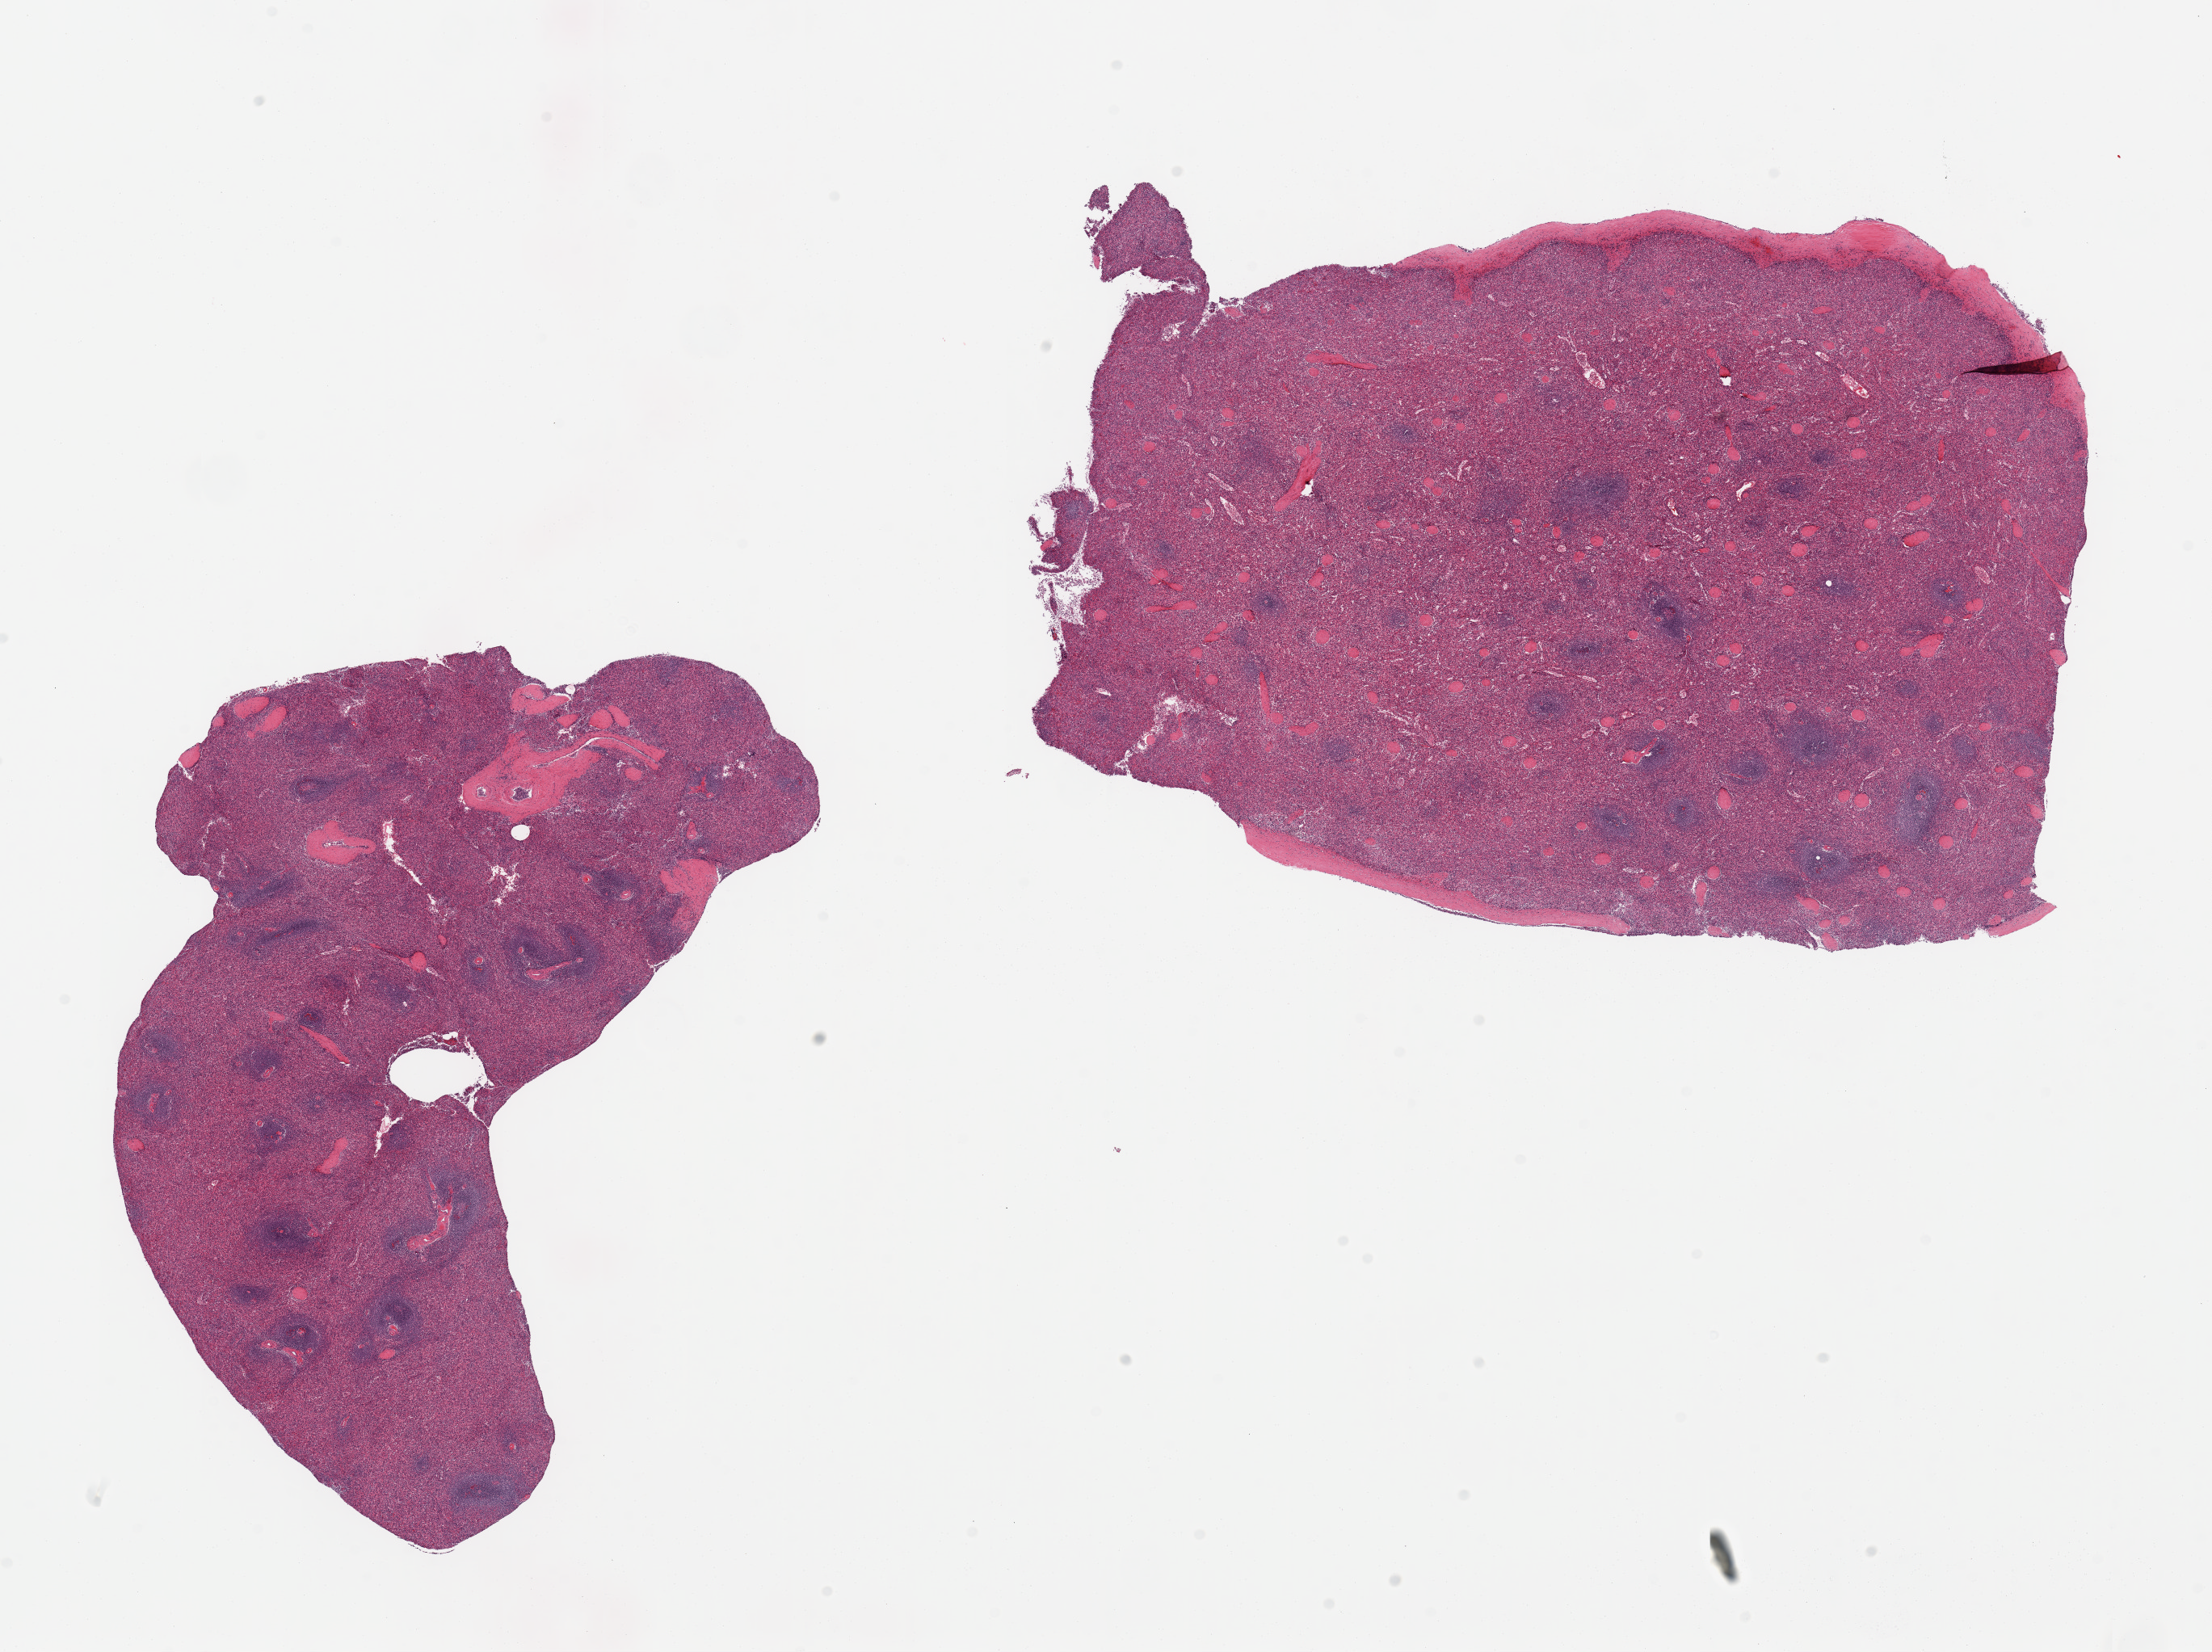
Digitized hematoxylin and eosin (H&E)-stained section, a low-resolution overview of the entire scanned area, about 21.7 x 16.2 mm (from a 20x scan), PAXgene-fixed, paraffin-embedded tissue, section of spleen (target tissue), donor tissue sample. Donor: male.
Pathologist's review note for this sample: 2 pieces.